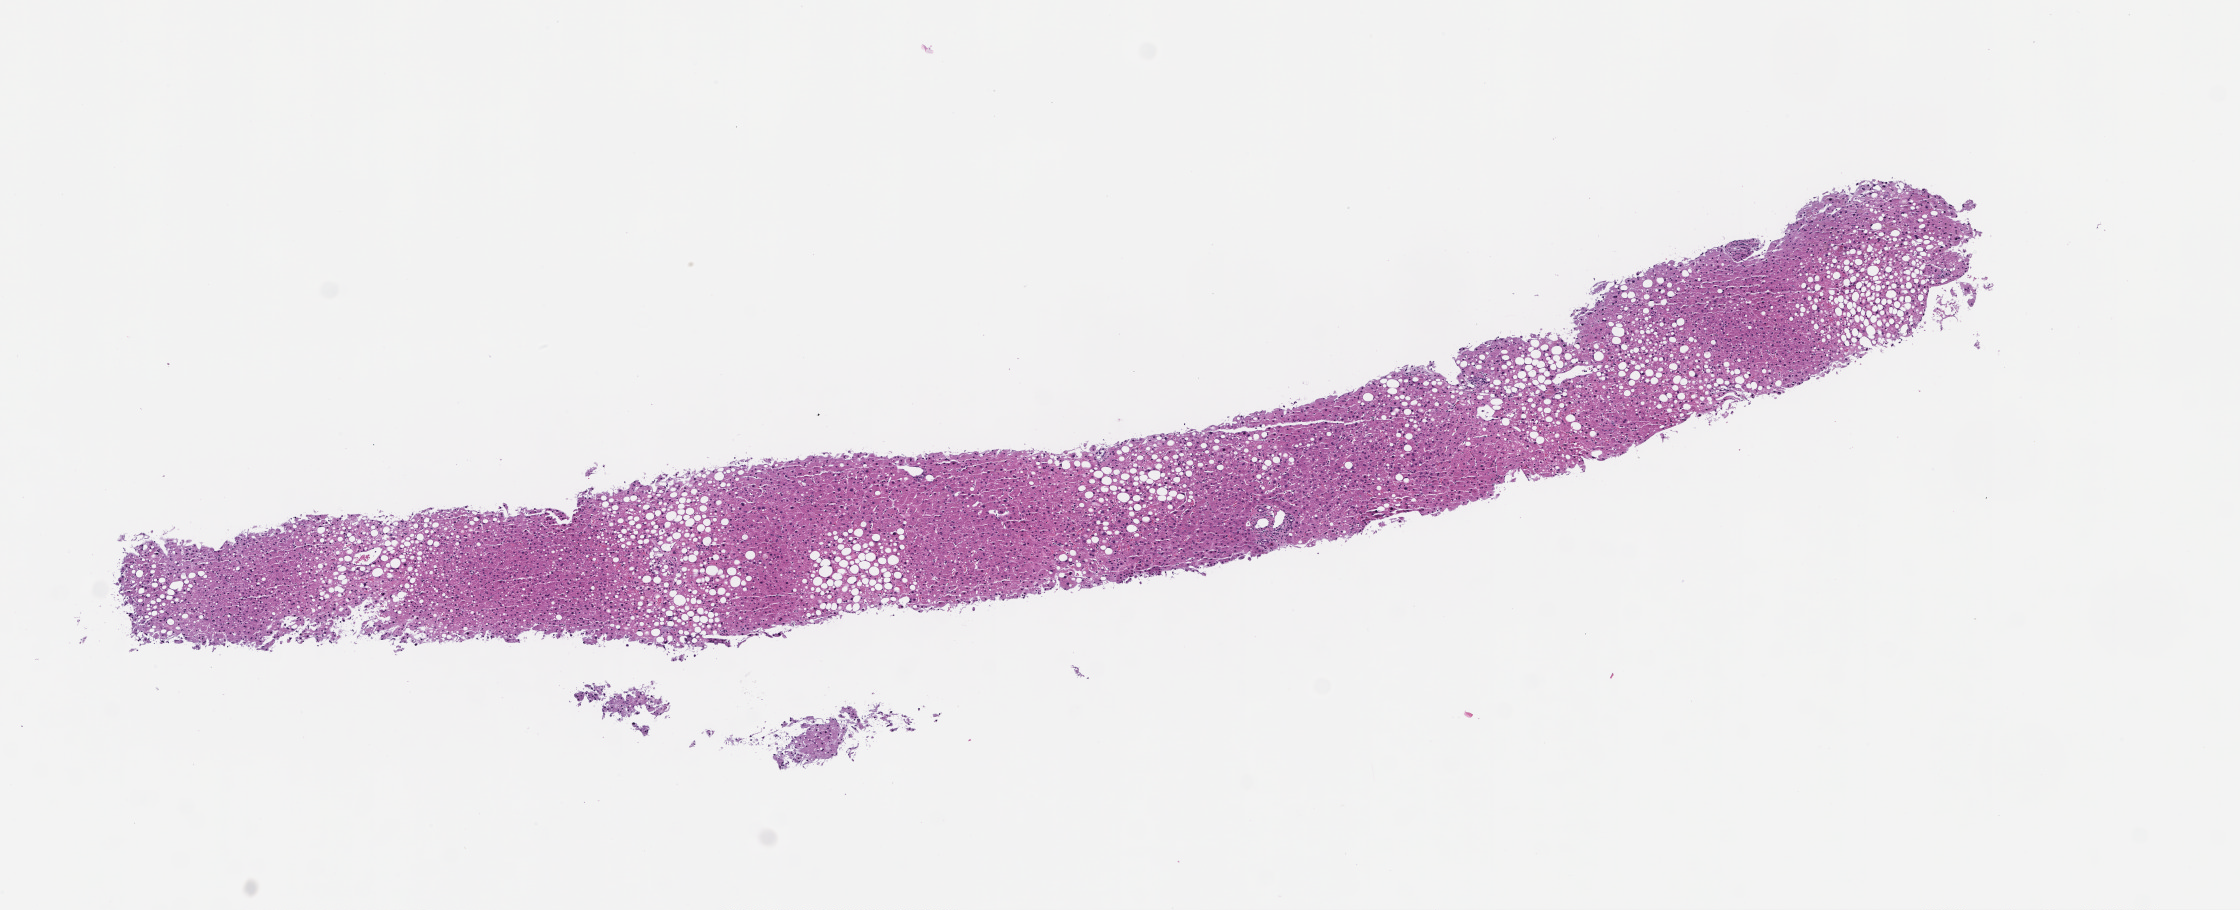
Digitized hematoxylin and eosin (H&E)-stained section, whole scanned area (about 9.0 x 3.7 mm) shown as a low-resolution overview. Formalin-fixed paraffin-embedded section. Specimen time point: collected at baseline (before treatment). Male patient.
• this section: metastatic tumor tissue
• patient diagnosis (primary): Melanoma